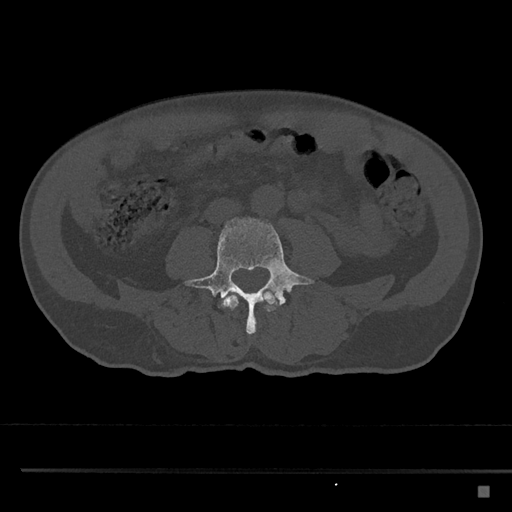
CT including the spine, one axial slice; slice 647 of 797 in the series (ordered by position); reconstruction kernel Br40s/3; bone window (W 1800 / L 400 HU); 0.5 mm slice thickness; 512 × 512 image matrix, field of view 391 × 391 mm. Male patient, age 59 years. From the clinical record (not read from this slice): primary cancer: prostate.
Outlined on this slice (semi-automatic segmentation, software-assisted and operator-edited):
- L3 vertebra: box from (x=221, y=291) to (x=278, y=319) px
- L4 vertebra: (x=184, y=218)–(x=314, y=337)